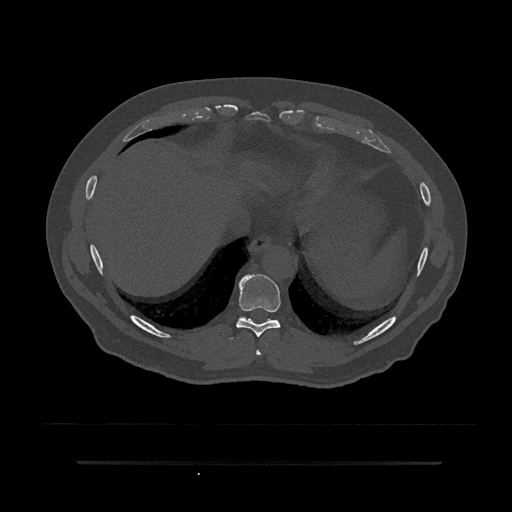
CT including the spine, one axial slice; position 370 of 797 along the scan axis; bone window (W 1800 / L 400 HU); 512 × 512 image matrix, field of view 464 × 464 mm. Male patient, age 59 years. Case-level facts recorded for this patient, not image findings: primary cancer: bile ducts.
Annotated regions visible in this slice (semi-automatically segmented with operator editing):
- T8 vertebra: bounding box [x1, y1, x2, y2] px = [256, 350, 262, 356]
- T9 vertebra: [230, 274, 281, 340]